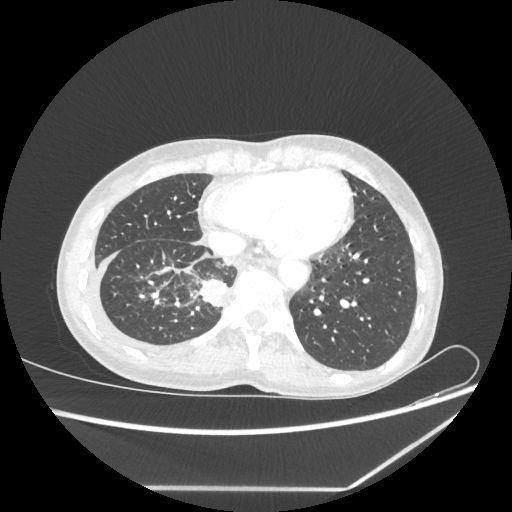
Chest CT, one axial slice. Position 67 of 237 along the scan axis. 80 kVp. Lung window (W 1500 / L -600 HU). 1.25 mm slice thickness. 512 × 512 image matrix. Female patient, age 59 years. Case-level facts recorded for this patient, not image findings: clinical TNM (as recorded): T1c N1 M1.
Structures marked on this image (rectangle marked by the reading radiologist):
- lung tumour (recorded histology: adenocarcinoma): box from (x=196, y=277) to (x=227, y=308) px